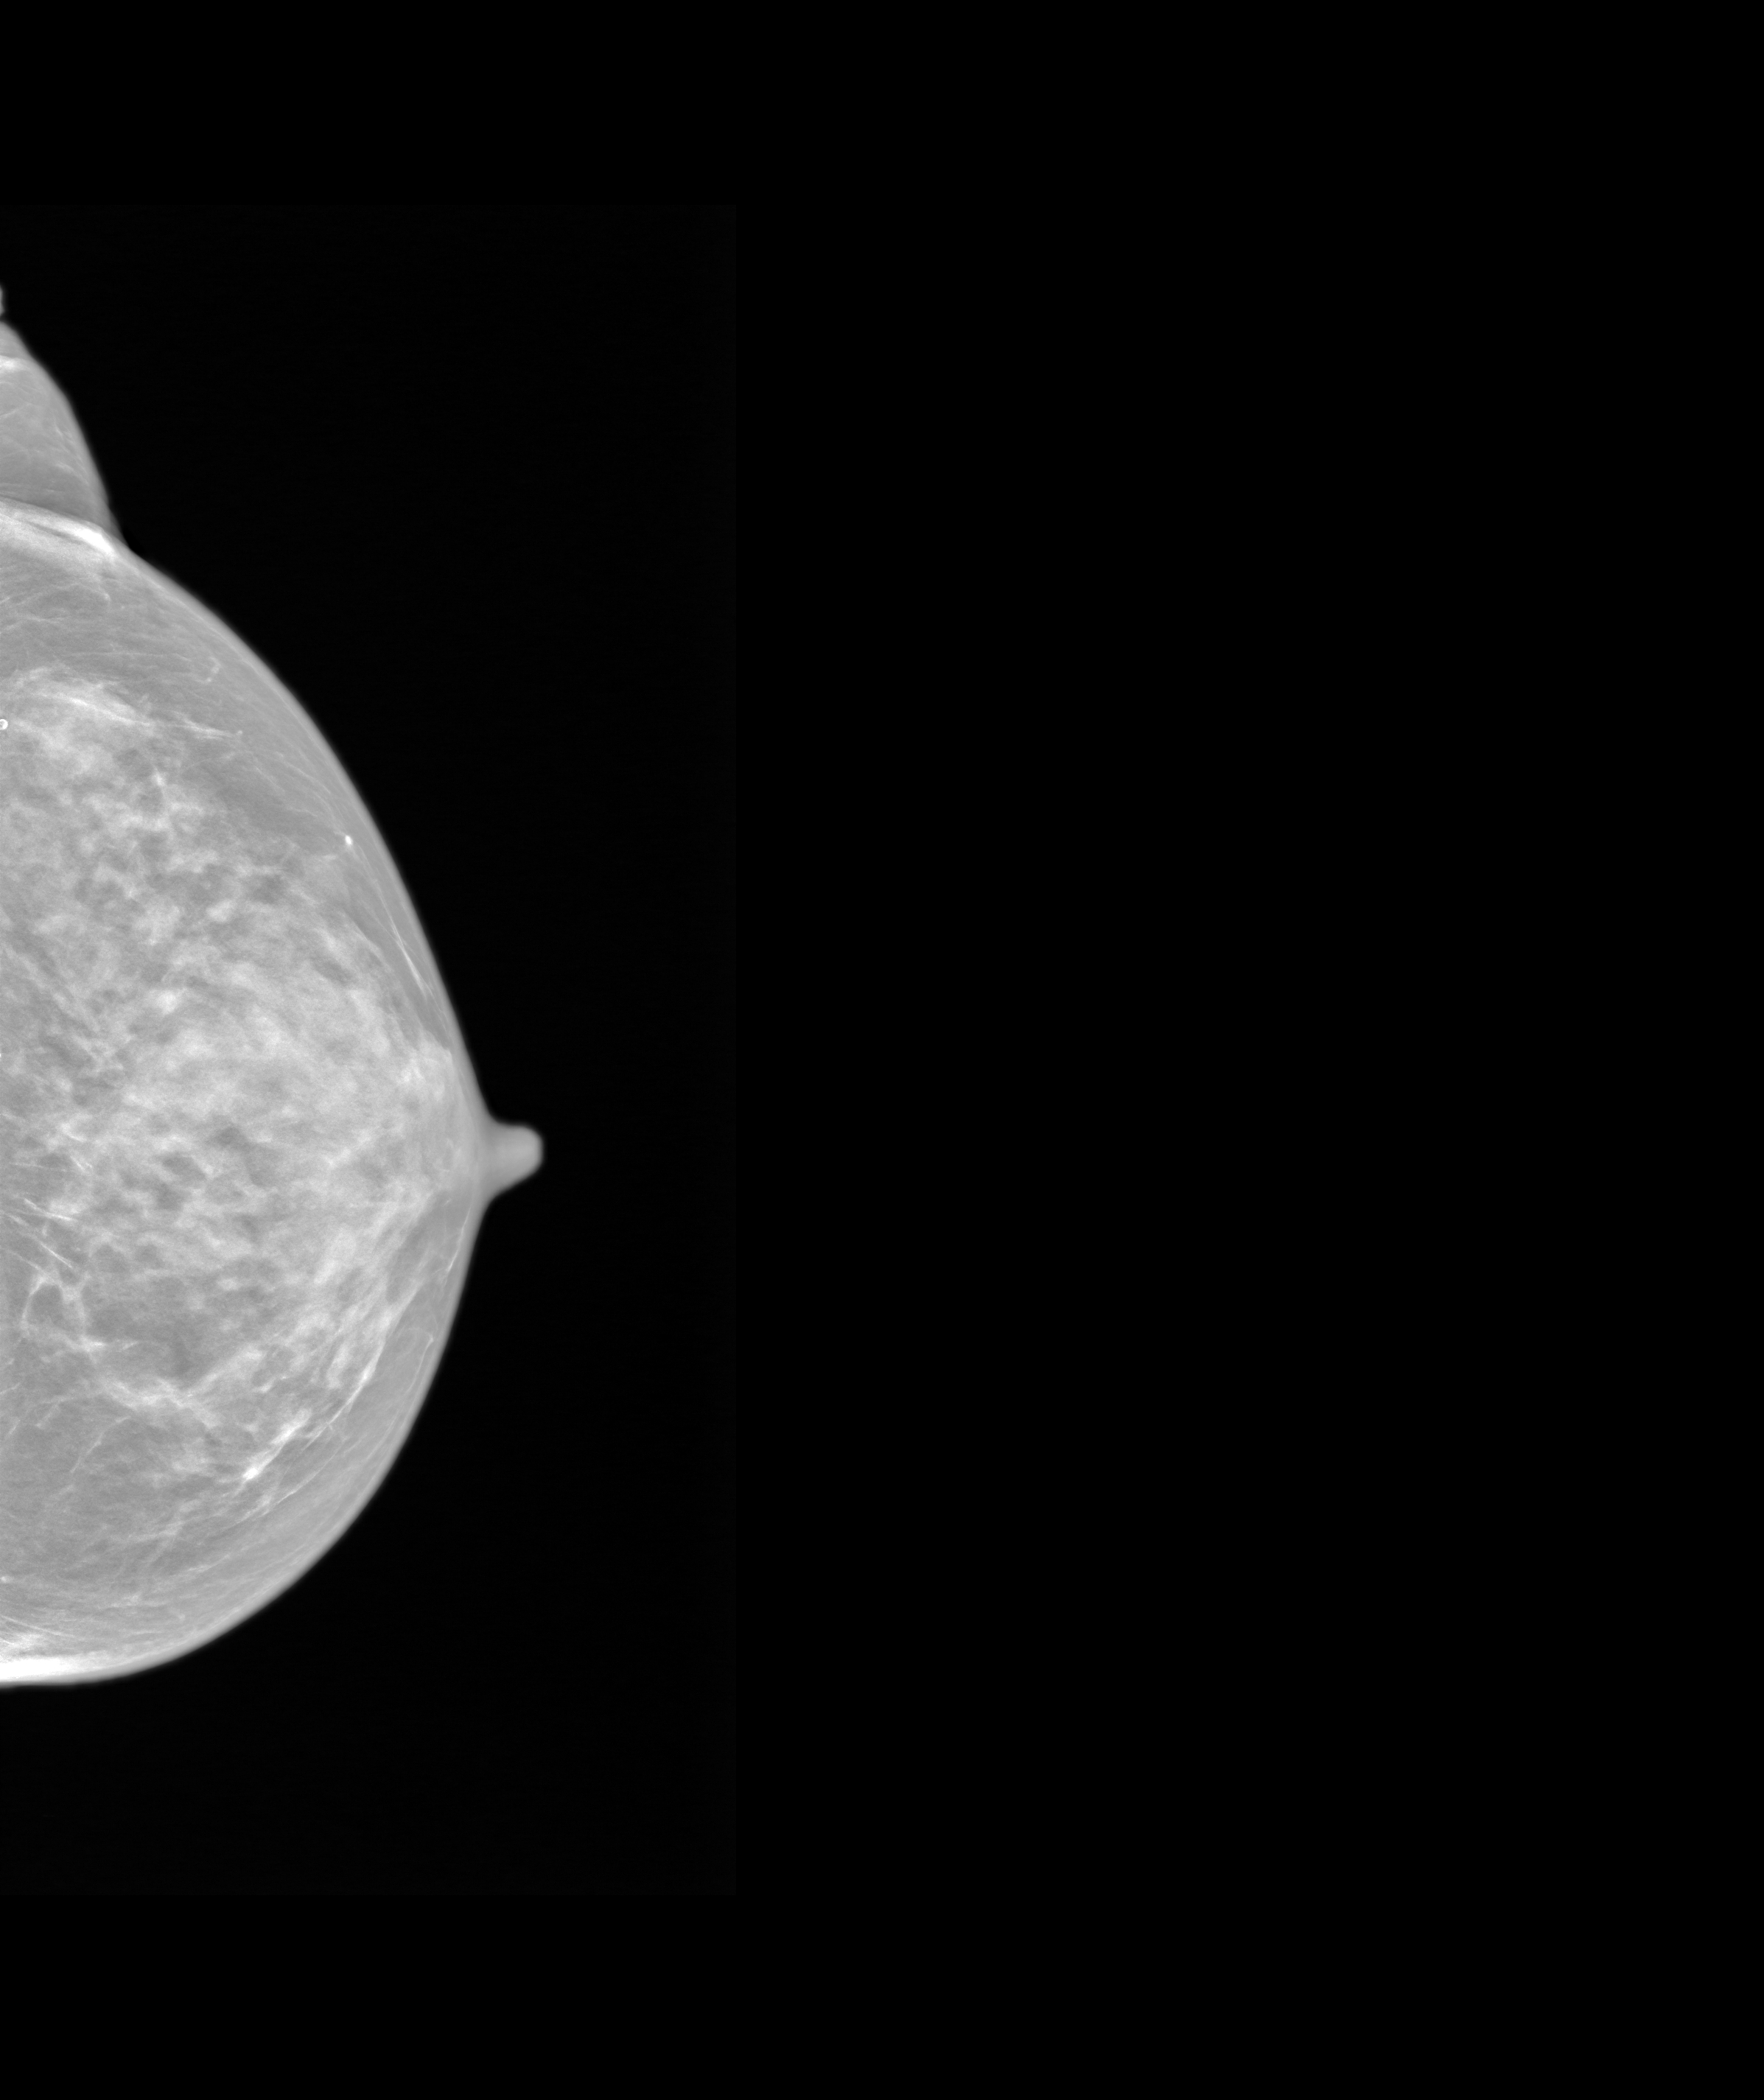
Annual screening mammography examination, system: SenoIris_1SP2(440). Female patient, age 68 years.
Image type: synthesized 2-D view from tomosynthesis. Breast: left. Projection: craniocaudal (CC) view.